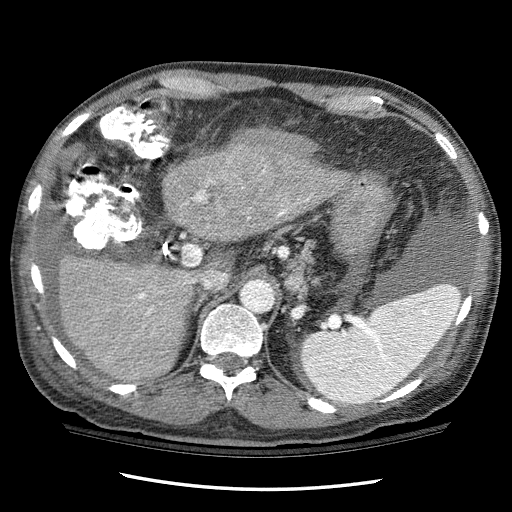
Contrast-enhanced abdominal CT (liver protocol), one axial slice. Slice 69 of 114 in the series (ordered by position). Reconstruction kernel STANDARD. One of 3 acquisitions stored at this slice position. Soft-tissue window (W 400 / L 40 HU). 2.5 mm slice thickness. 512 × 512 image matrix, field of view 360 × 360 mm. From the clinical record (not read from this slice): diagnosis: hepatocellular carcinoma (patient treated with transarterial chemoembolisation; whether this scan precedes or follows treatment is not stated here); TNM stage (as recorded): Stage-I; Child-Pugh class: C.
Outlined on this slice (semi-automatic segmentation, software-assisted and operator-edited):
- liver parenchyma outside the tumour (the mass and vessels are separate outlines, so this box may not span the whole liver): bounding box [x1, y1, x2, y2] px = [58, 144, 350, 382]
- mass: [219, 129, 322, 186]
- liver vessels: [138, 180, 309, 315]